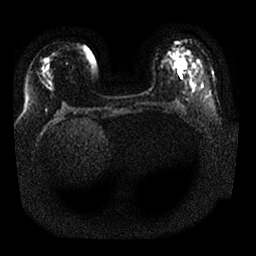
Breast MRI, one axial slice. Position 8 of 25 along the scan axis. Diffusion-weighted series; image 2 of 4 stored at this slice position (different b-values; order by instance number). 1.5 T. 4 mm slice thickness. 256 × 256 image matrix. Female patient.
Annotated regions visible in this slice (manually delineated by an expert):
- tumour on diffusion-weighted imaging: box from (x=175, y=58) to (x=186, y=74) px